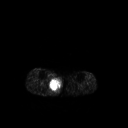
FDG PET of an extremity soft-tissue mass (from a PET/CT study), one axial slice. Slice 142 of 267 in the series (ordered by position). 128 × 128 image matrix, field of view 500 × 500 mm. Patient: male, 69 years. Case-level facts recorded for this patient, not image findings: histological type: pleiomorphic liposarcoma; grade: high; site of the primary tumour: right calf.
Structures marked on this image (expert contour drawn on MRI and transferred to this co-registered scan by the dataset authors):
- gross tumour volume including surrounding oedema: bounding box <49,76,61,91> (left, top, right, bottom; pixels)
- gross tumour volume (mass): <50,79,61,89>